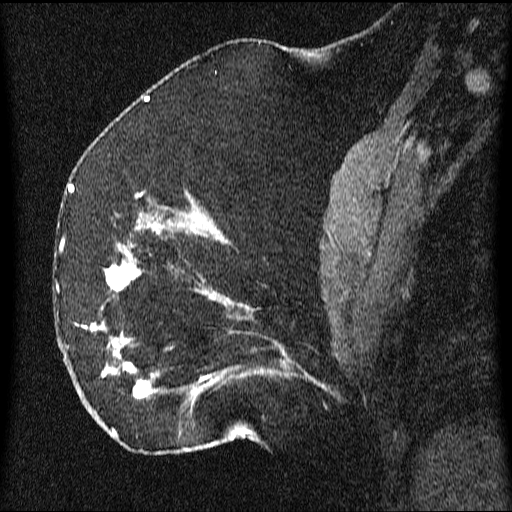
Breast MRI (dynamic contrast-enhanced), one sagittal slice. Slice 25 of 64 in the series (ordered by position). Dynamic contrast-enhanced series, image 2 of 3 at this slice position (ordered by acquisition). 1.5 T. TE 4.2 ms, TR 9.1 ms. 2.2 mm slice thickness. 512 × 512 image matrix, field of view 180 × 180 mm. Female patient, age 52 years.
Annotated regions visible in this slice (semi-automatically segmented with operator editing):
- analysis volume of interest (the breast-tissue region the enhancement analysis was run in; not a lesion): bounding box <61,203,350,438> (left, top, right, bottom; pixels)
- tumour enhancement mask (voxels above the 70 % enhancement threshold inside the analysis volume of interest): <62,203,286,437>